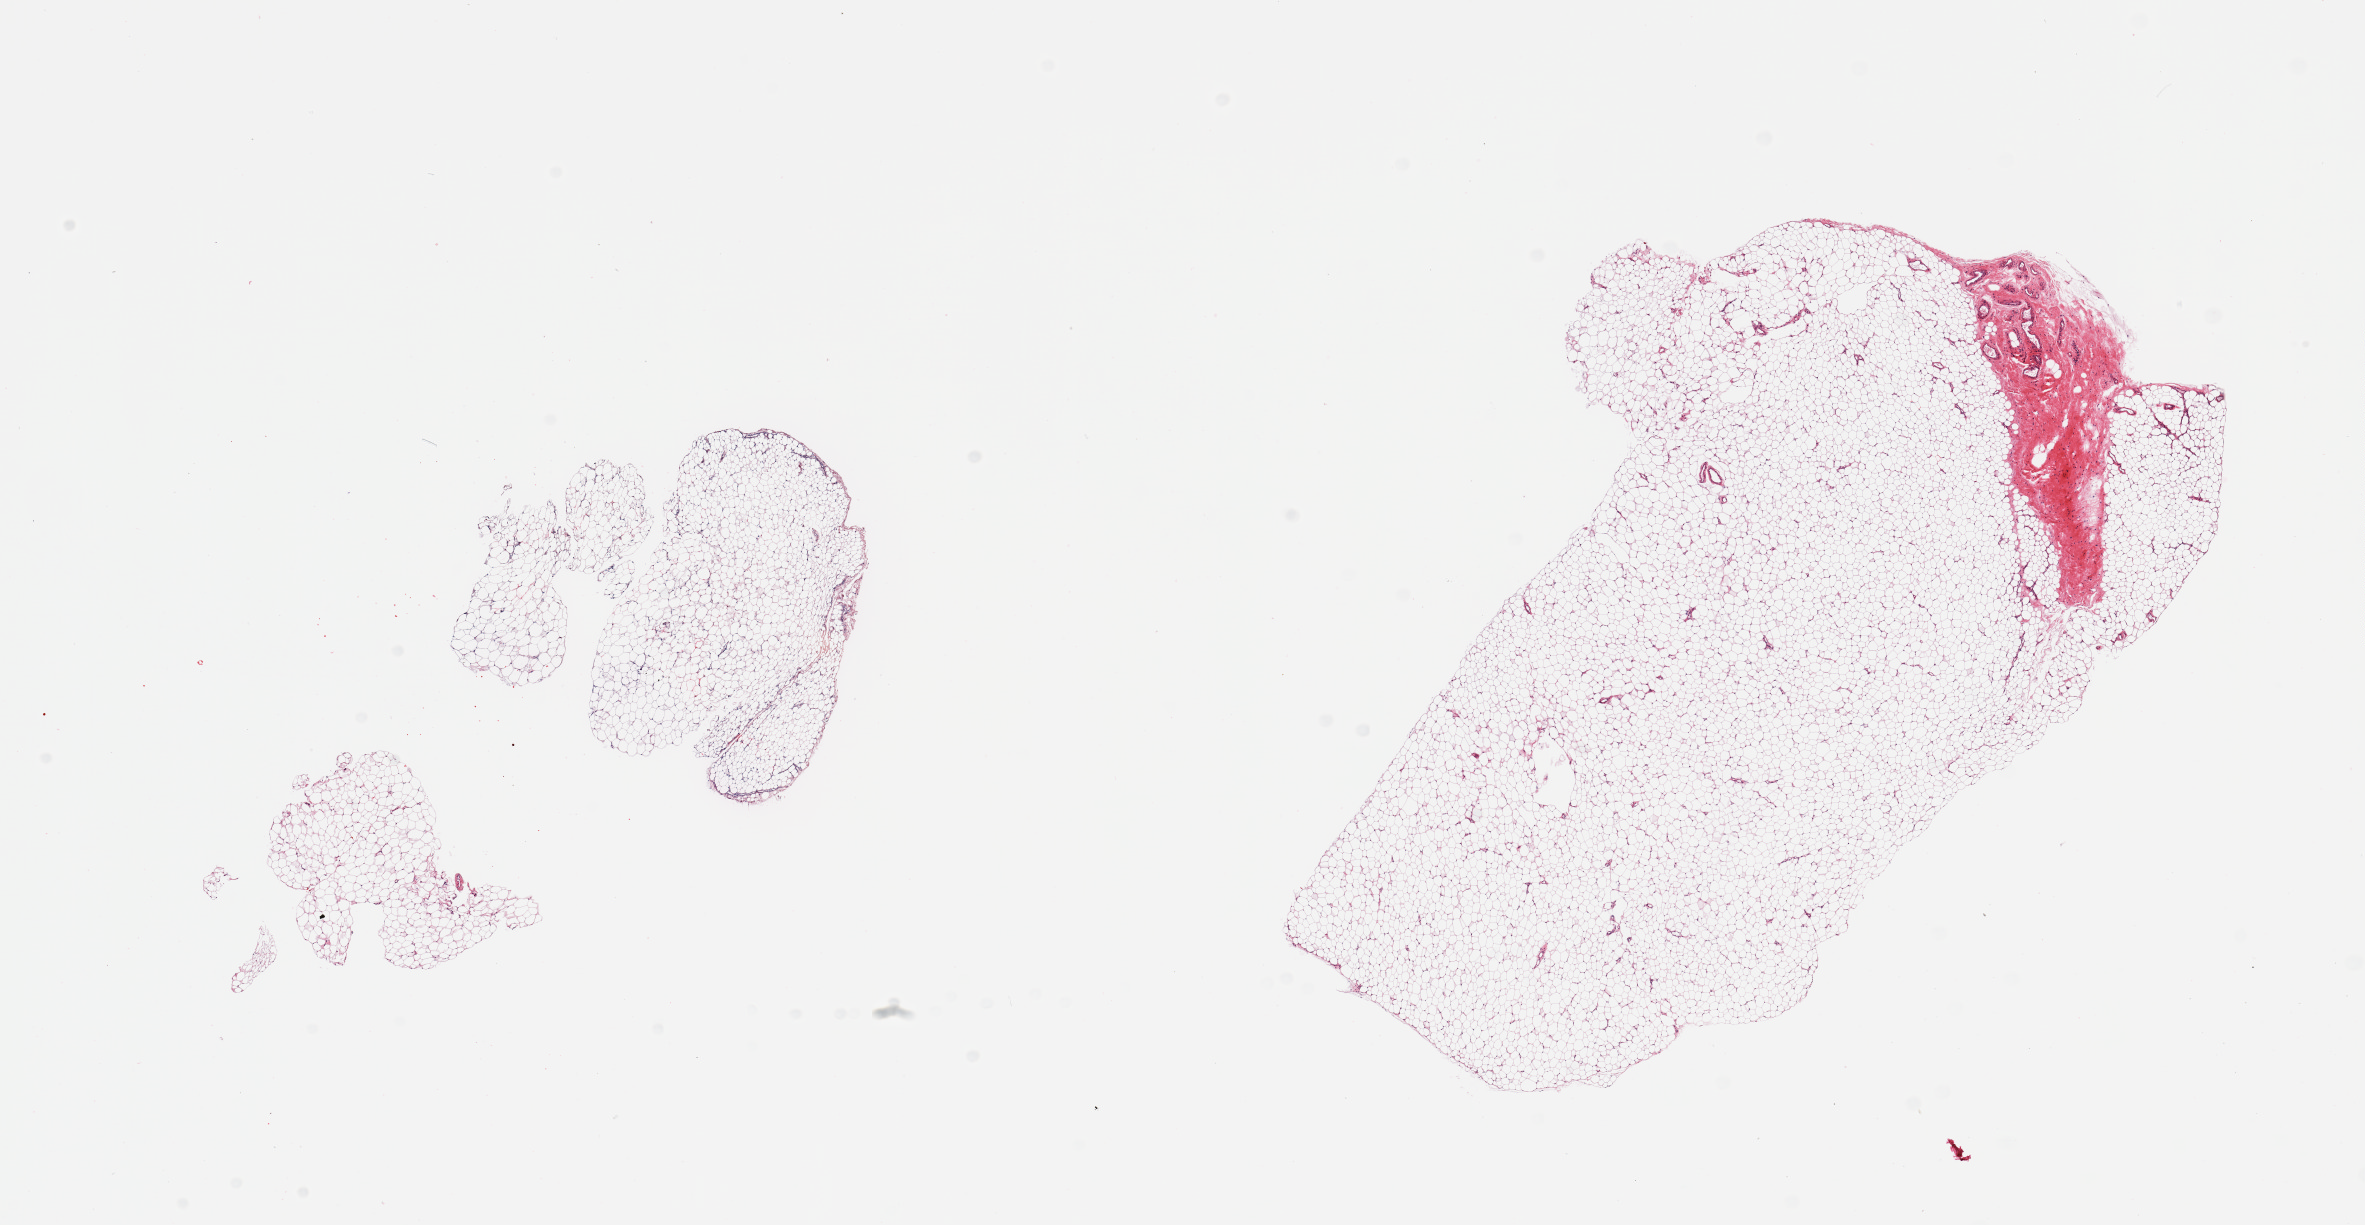
H&E whole-slide image — shown as a low-resolution overview of the whole scanned area (about 18.7 x 9.7 mm); PAXgene-fixed, paraffin-embedded tissue; section of adipose tissue (target tissue); donor tissue sample. Donor: female.
Review note (as recorded): 2 pieces; 10% fibrous content in 1 piece.